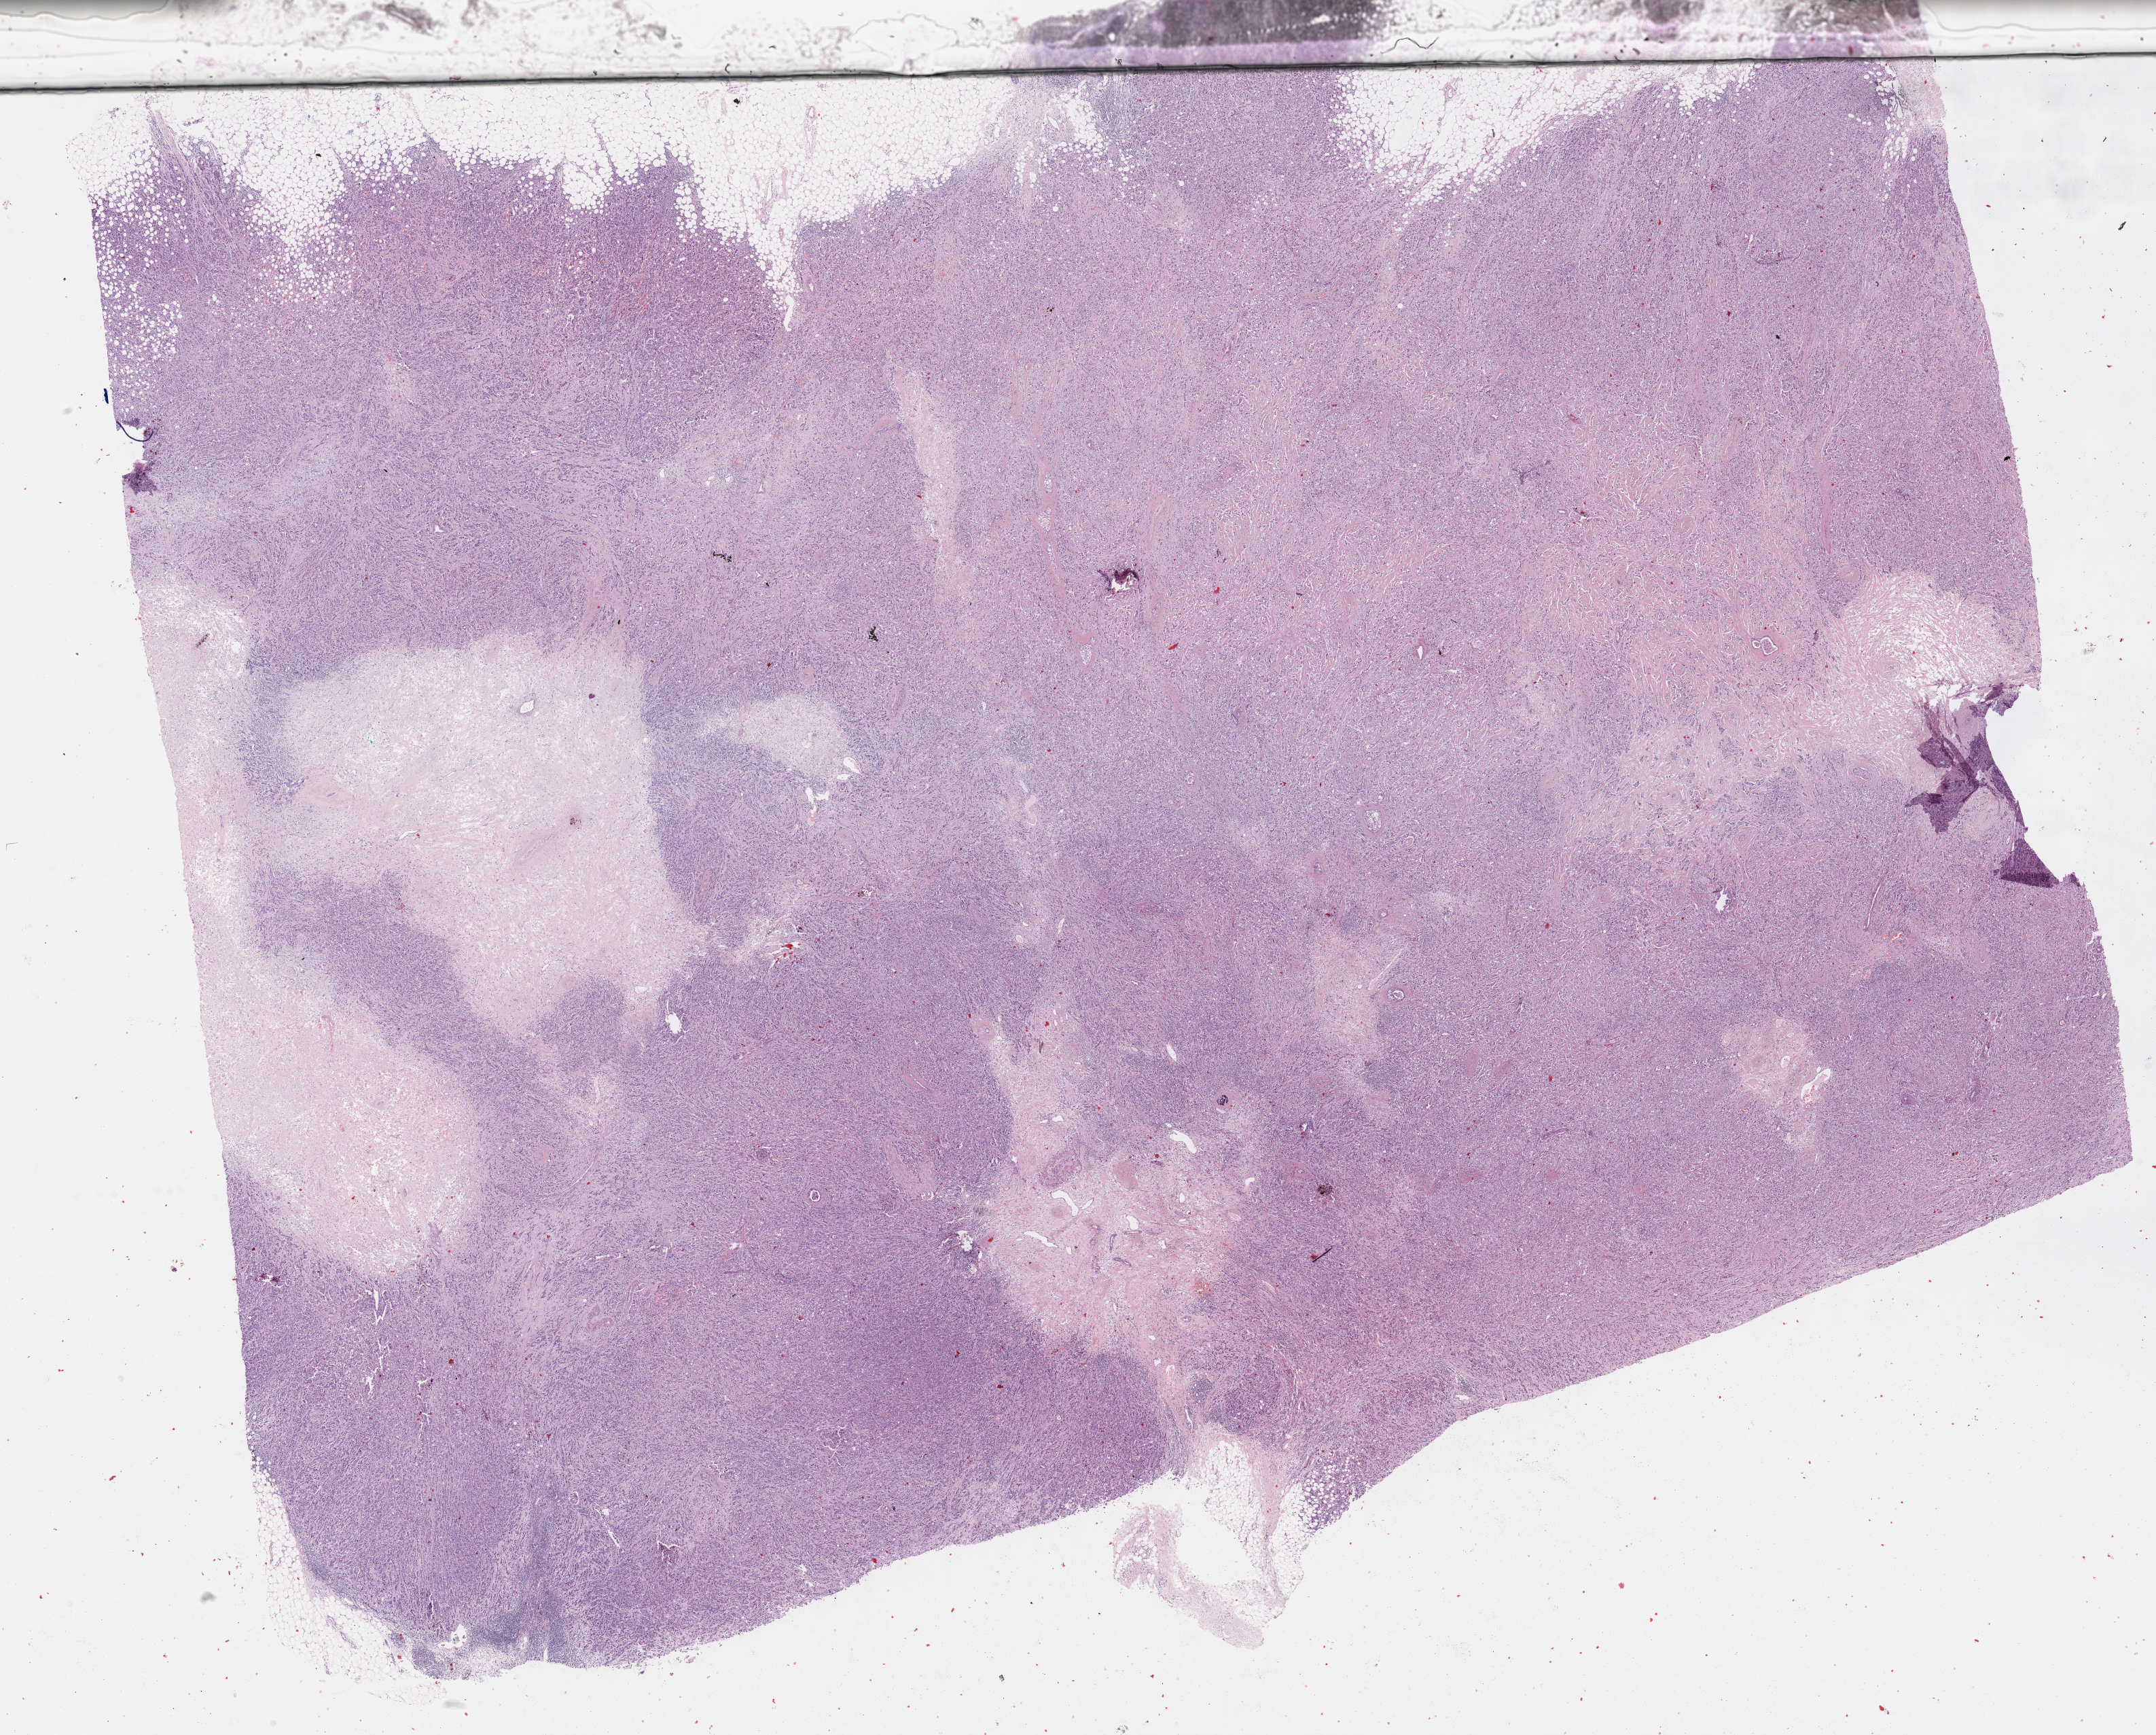
H&E-stained whole-slide image, a low-resolution overview of the entire scanned area, about 25.7 x 20.7 mm (slide scanned at 40x). Formalin-fixed paraffin-embedded (FFPE) diagnostic section. Primary tumour sample from the breast. Female, age 81 years at initial diagnosis.
AJCC pathologic stage: IIIC. Lymph nodes positive (case pathology): 14 of 16 examined. Diagnosis: Infiltrating duct carcinoma, NOS.